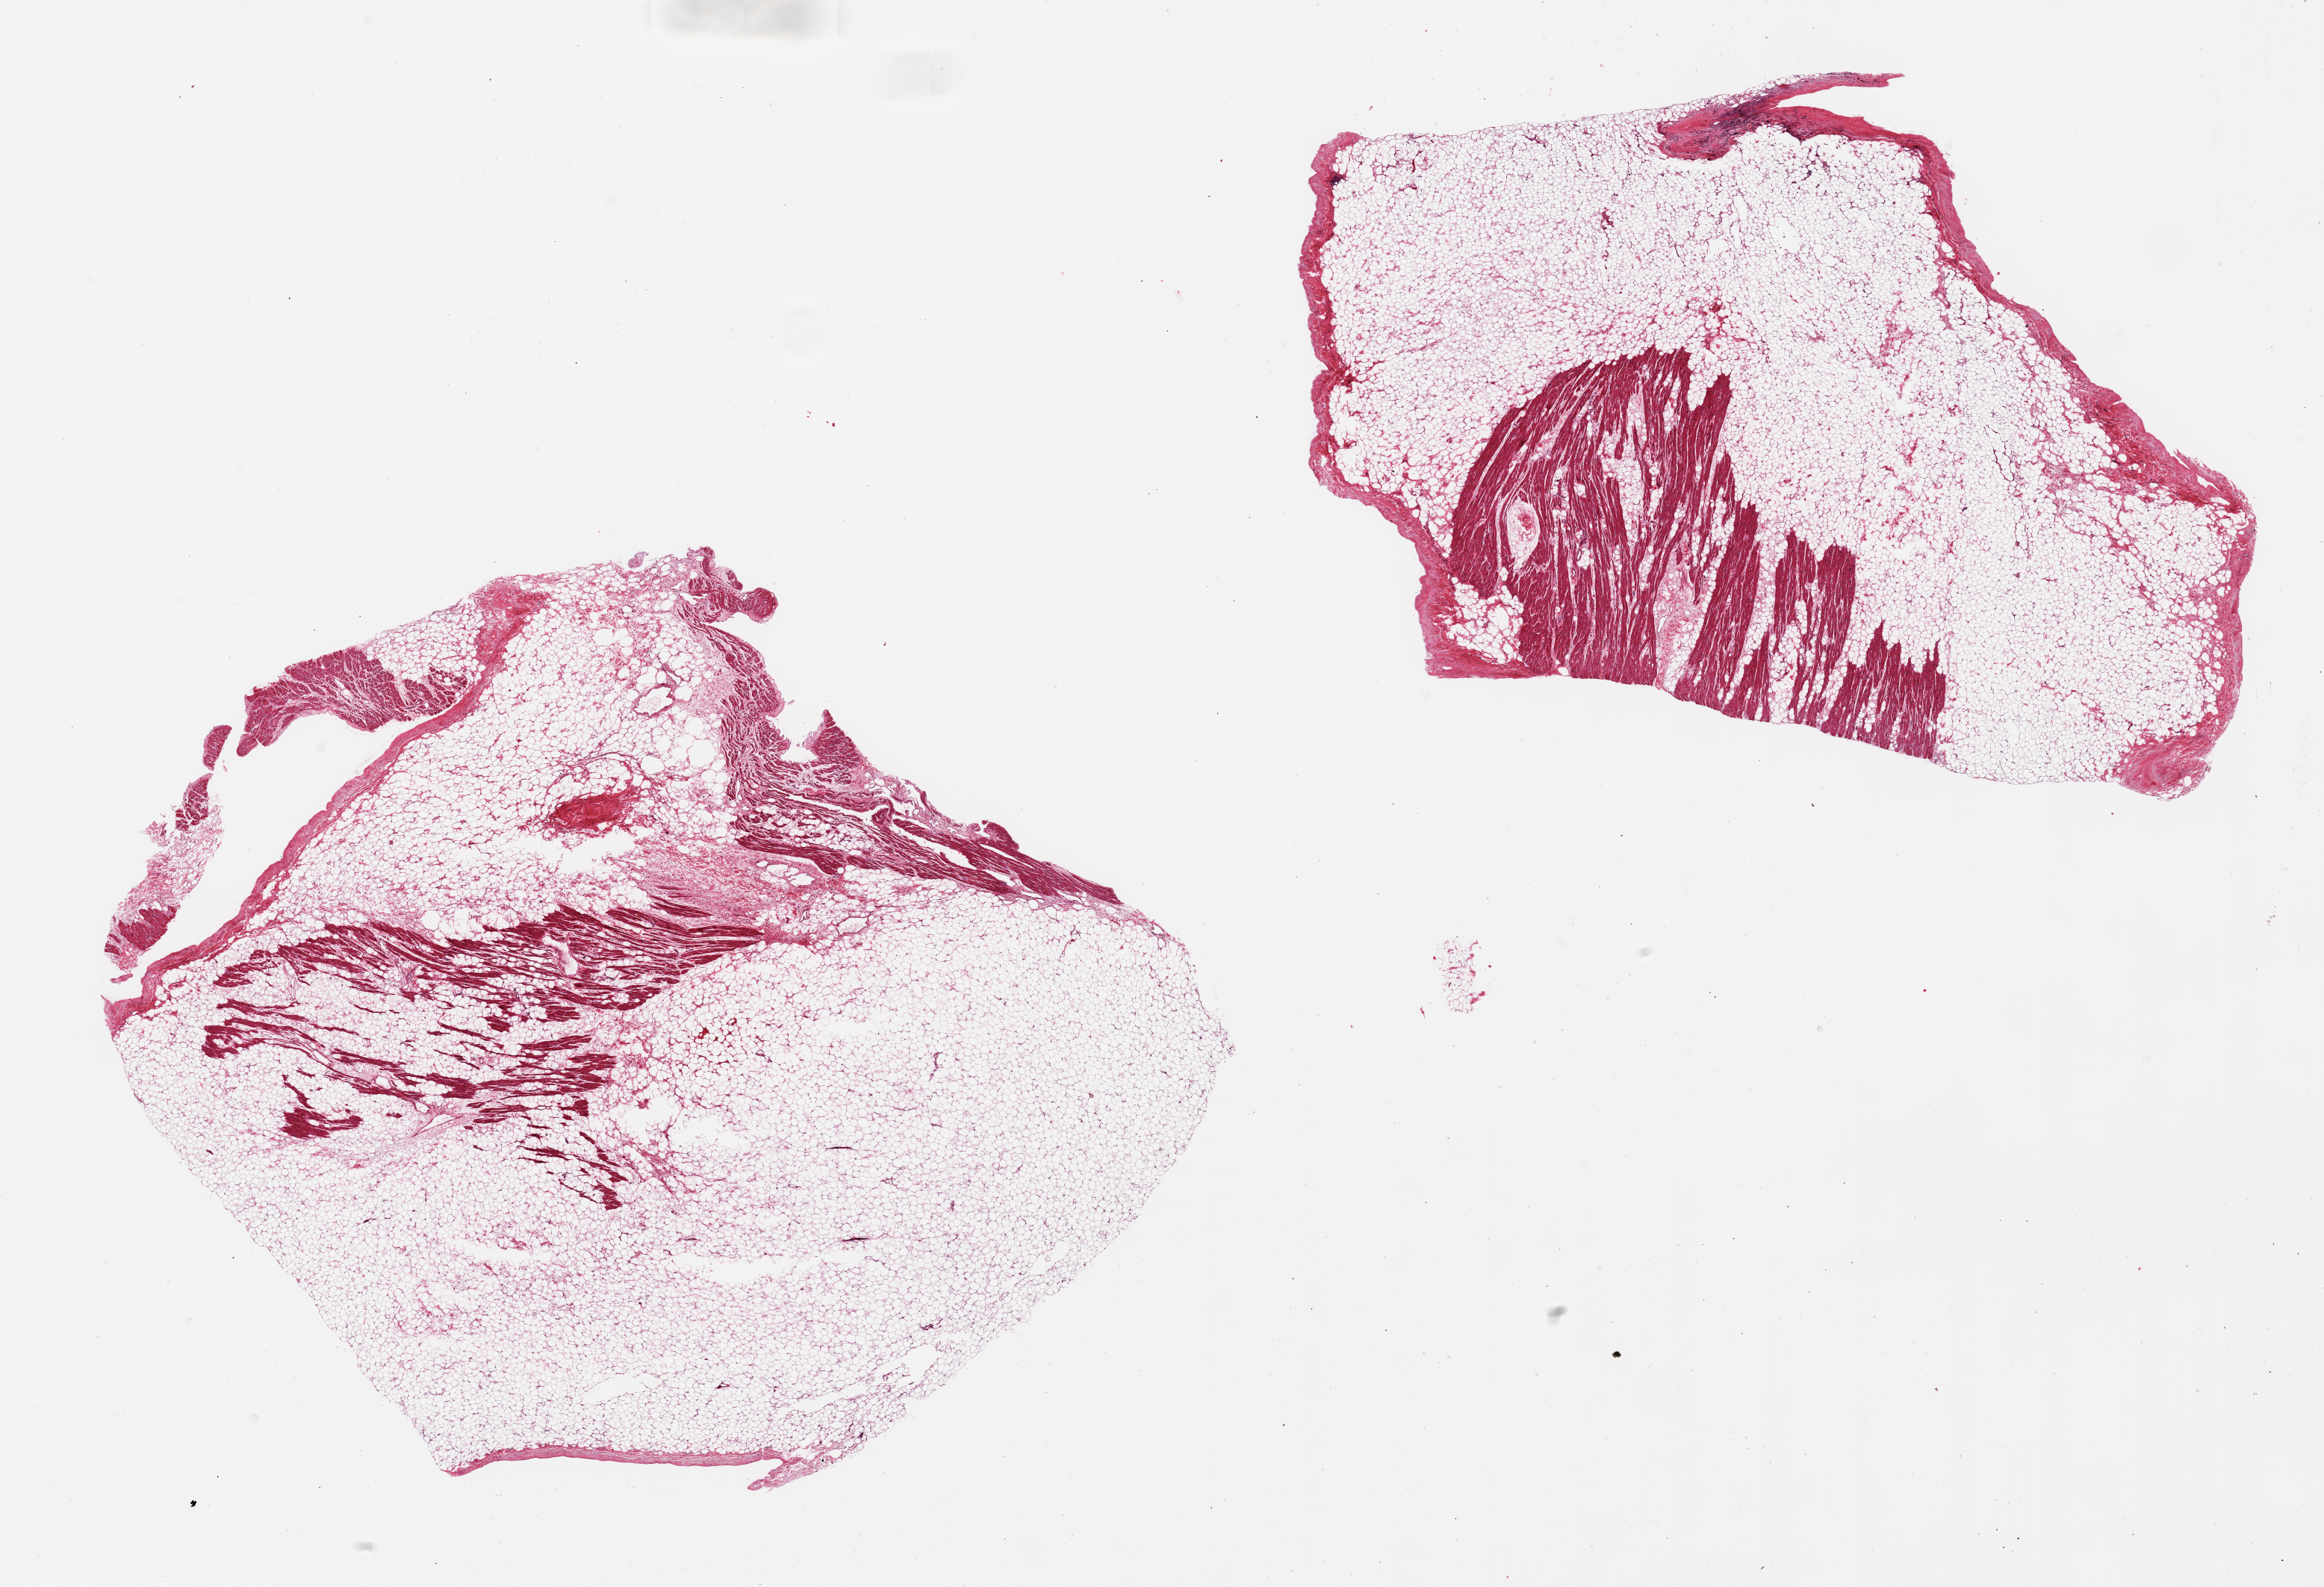
Haematoxylin and eosin whole-slide image, brightfield — shown as a low-resolution overview of the whole scanned area (about 24.6 x 16.8 mm).
Specimen: PAXgene-fixed paraffin-embedded (PFPE) section; target tissue: auricular appendage; donor tissue sample.